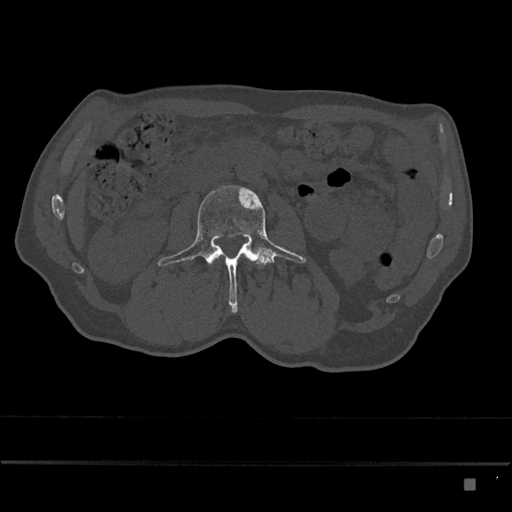
CT including the spine, one axial slice. Slice 414 of 797 in the series (ordered by position). Reconstruction kernel Br40s/3. Bone window (W 1800 / L 400 HU). 0.5 mm slice thickness. 512 × 512 image matrix, field of view 390 × 390 mm. Male patient, age 72 years. From the clinical record (not read from this slice): primary cancer: prostate.
Outlined on this slice (semi-automatically segmented with operator editing):
- L2 vertebra: bounding box (x1, y1, x2, y2) in pixels: (216, 257, 219, 259)
- L3 vertebra: (158, 185, 306, 313)